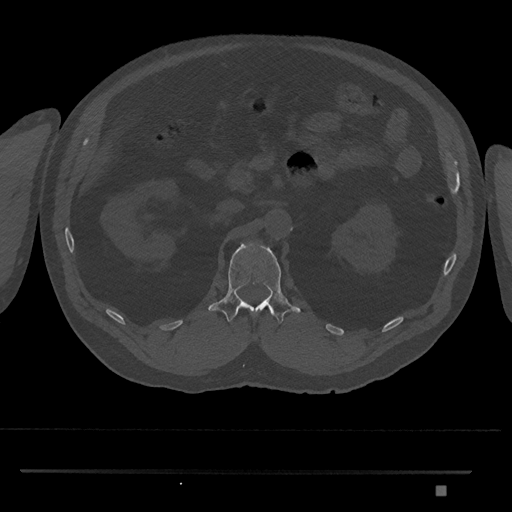
CT including the spine, one axial slice. Slice 828 of 1134 in the series (ordered by position). Reconstruction kernel Br40s/3. Bone window (W 1800 / L 400 HU). 0.5 mm slice thickness. 512 × 512 image matrix, field of view 429 × 429 mm. Male patient, age 65 years. Case-level facts recorded for this patient, not image findings: primary cancer: prostate.
Structures marked on this image (semi-automatic segmentation, software-assisted and operator-edited):
- L1 vertebra: bounding box [x1, y1, x2, y2] px = [208, 242, 301, 324]